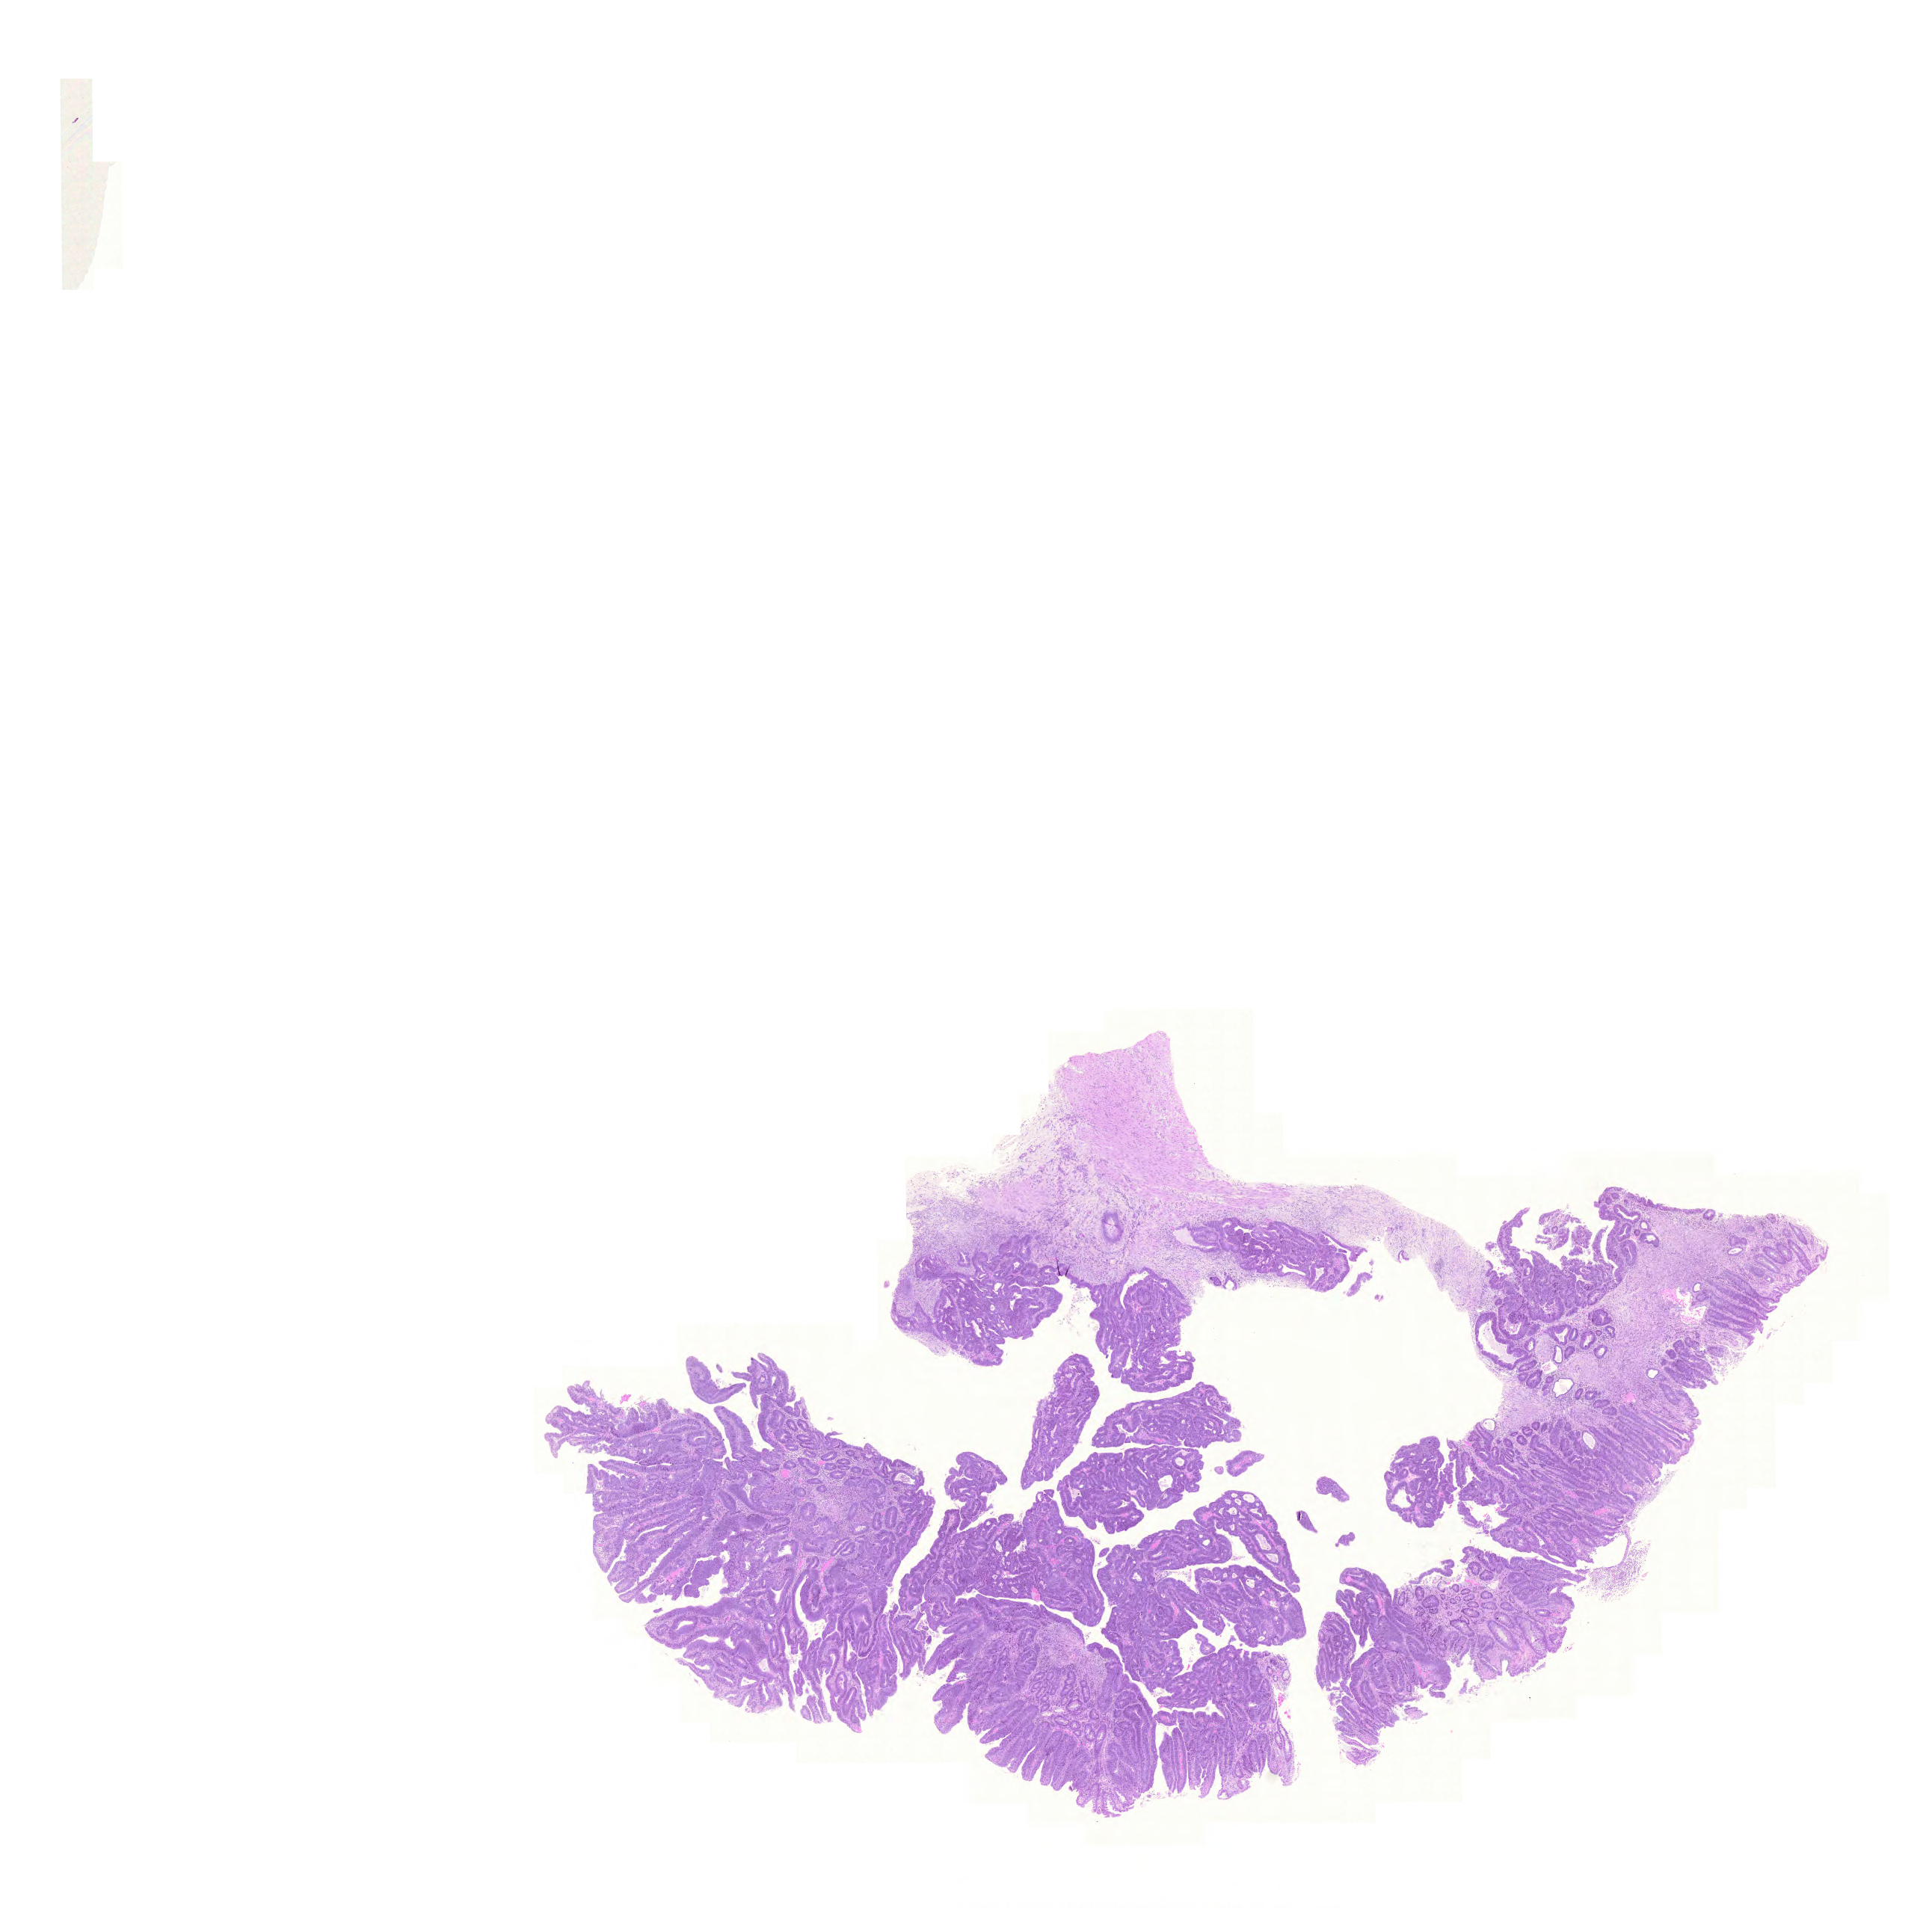
Whole-slide histology image, Hematoxylin and eosin (H&E) stained — a low-resolution overview of the entire scanned area, about 19.2 x 19.0 mm (from a 20x scan), formalin-fixed paraffin-embedded (FFPE) diagnostic section, primary tumour sample from the colon. Female patient; age at initial diagnosis 36 years.
Lymph nodes positive (case pathology): 0 of 22 examined. Diagnosis: Adenocarcinoma, NOS. AJCC pathologic stage: I (5th edition).